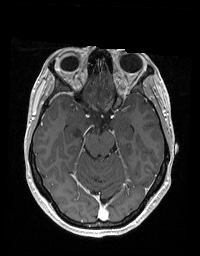
Brain MRI from a brain-tumour surgery series, one axial slice. Position 119 of 192 along the scan axis. T1-weighted post-contrast. 200 × 256 image matrix, field of view 195 × 250 mm. Case-level facts recorded for this patient, not image findings: histopathology: Glioblastoma; WHO grade: 2.
Outlined on this slice (expert manual segmentation):
- tumour: bounding box <72,113,102,137> (left, top, right, bottom; pixels)